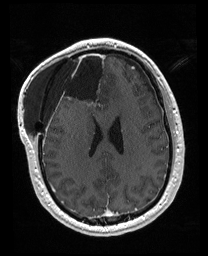
Brain MRI from a brain-tumour surgery series, one axial slice; position 71 of 176 along the scan axis; T1-weighted post-contrast; 208 × 256 image matrix, field of view 208 × 256 mm. From the clinical record (not read from this slice): histopathology: Astrocytoma; WHO grade: 4; IDH mutation: yes; tumour location: Right Orbitofrontal Anterior Temporal Insular.
Structures marked on this image (manually delineated by an expert):
- previous resection cavity: bounding box (x1, y1, x2, y2) in pixels: (56, 52, 106, 111)